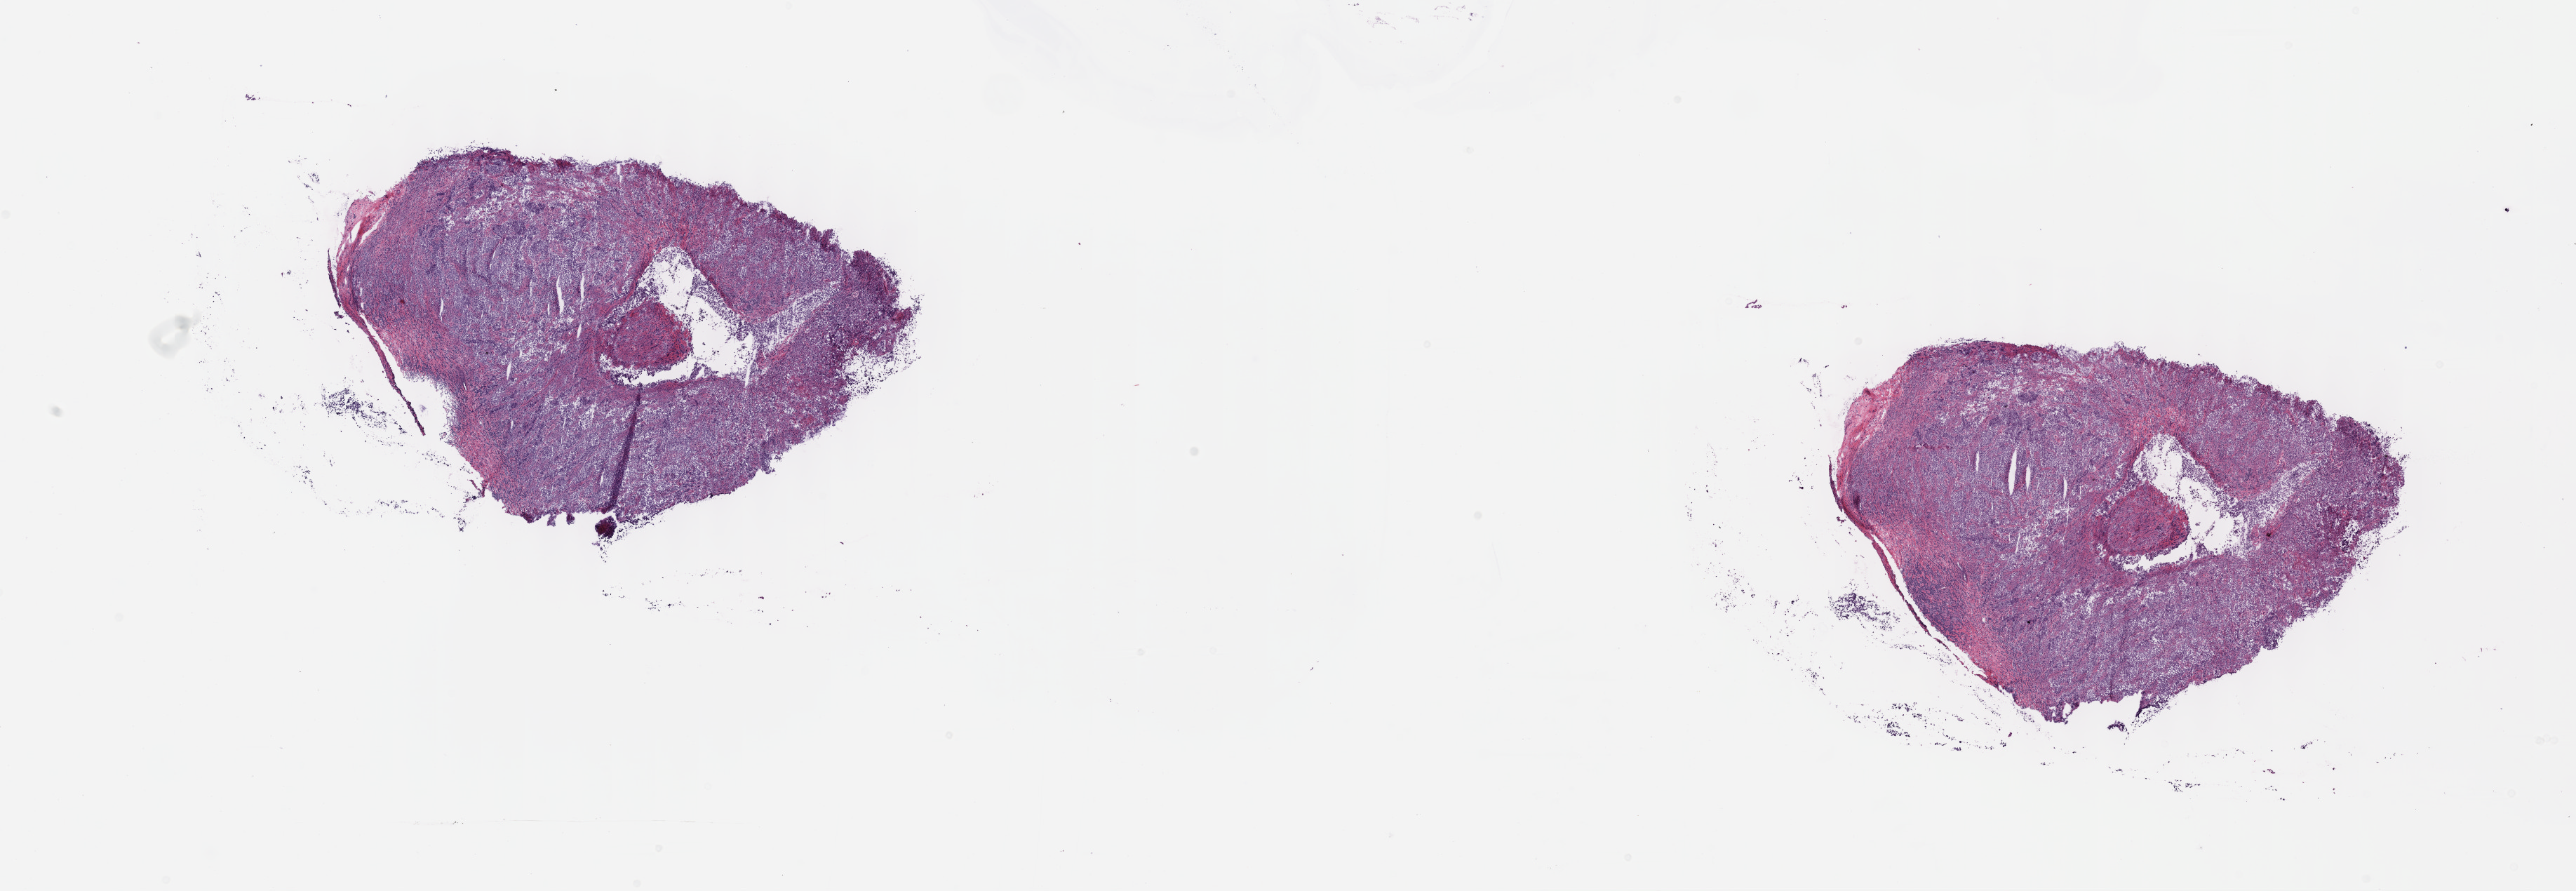
Whole-slide histology image, H&E-stained, shown as a low-resolution overview of the whole scanned area (about 29.7 x 10.3 mm). Frozen section from the top of the tissue portion. Primary tumour sample from the testis. Male, age 35 years at initial diagnosis. Composition of this section per pathologist review: tumour cells 70%, tumour nuclei 70%, normal cells 0%, stromal cells 25%, necrosis 5%. Infiltration values recorded for this section: lymphocyte infiltration 60%, monocyte infiltration 10%, neutrophil infiltration 10%.
AJCC pathologic stage: IA. Diagnosis: Seminoma, NOS.